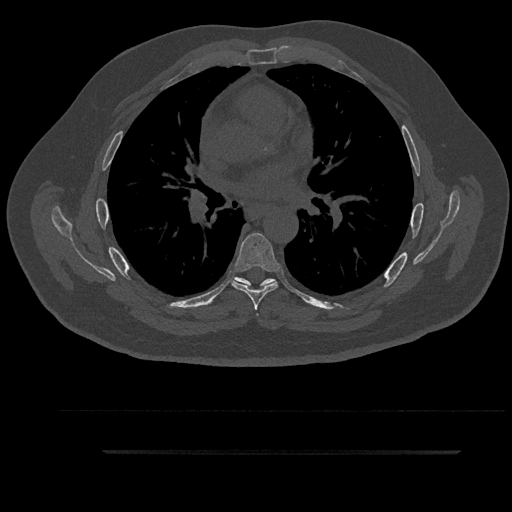
CT including the spine, one axial slice. Slice 567 of 797 in the series (ordered by position). Reconstruction kernel Br40s/3. 120 kVp. Bone window (W 1800 / L 400 HU). 0.5 mm slice thickness. 512 × 512 image matrix, field of view 432 × 432 mm. Male patient, age 63 years. Case-level facts recorded for this patient, not image findings: primary cancer: renal; vertebrae with lytic lesions (as recorded): T8.
Structures marked on this image (semi-automatically segmented with operator editing):
- T5 vertebra: box from (x=235, y=277) to (x=266, y=315) px
- T6 vertebra: (x=232, y=233)–(x=280, y=311)
- T7 vertebra: (x=239, y=278)–(x=276, y=286)